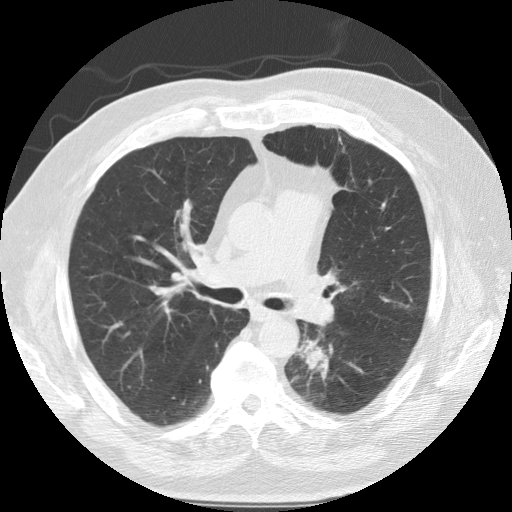
Low-dose screening chest CT, one axial slice. Position 73 of 124 along the scan axis. Reconstruction kernel STANDARD. 120 kVp. Lung window (W 1500 / L -600 HU). 2.5 mm slice thickness. 512 × 512 image matrix, field of view 360 × 360 mm.
Outlined on this slice (outlined manually by an expert reader):
- lesion 1 (tumor, lower lobe of left lung): box from (x=297, y=340) to (x=329, y=383) px